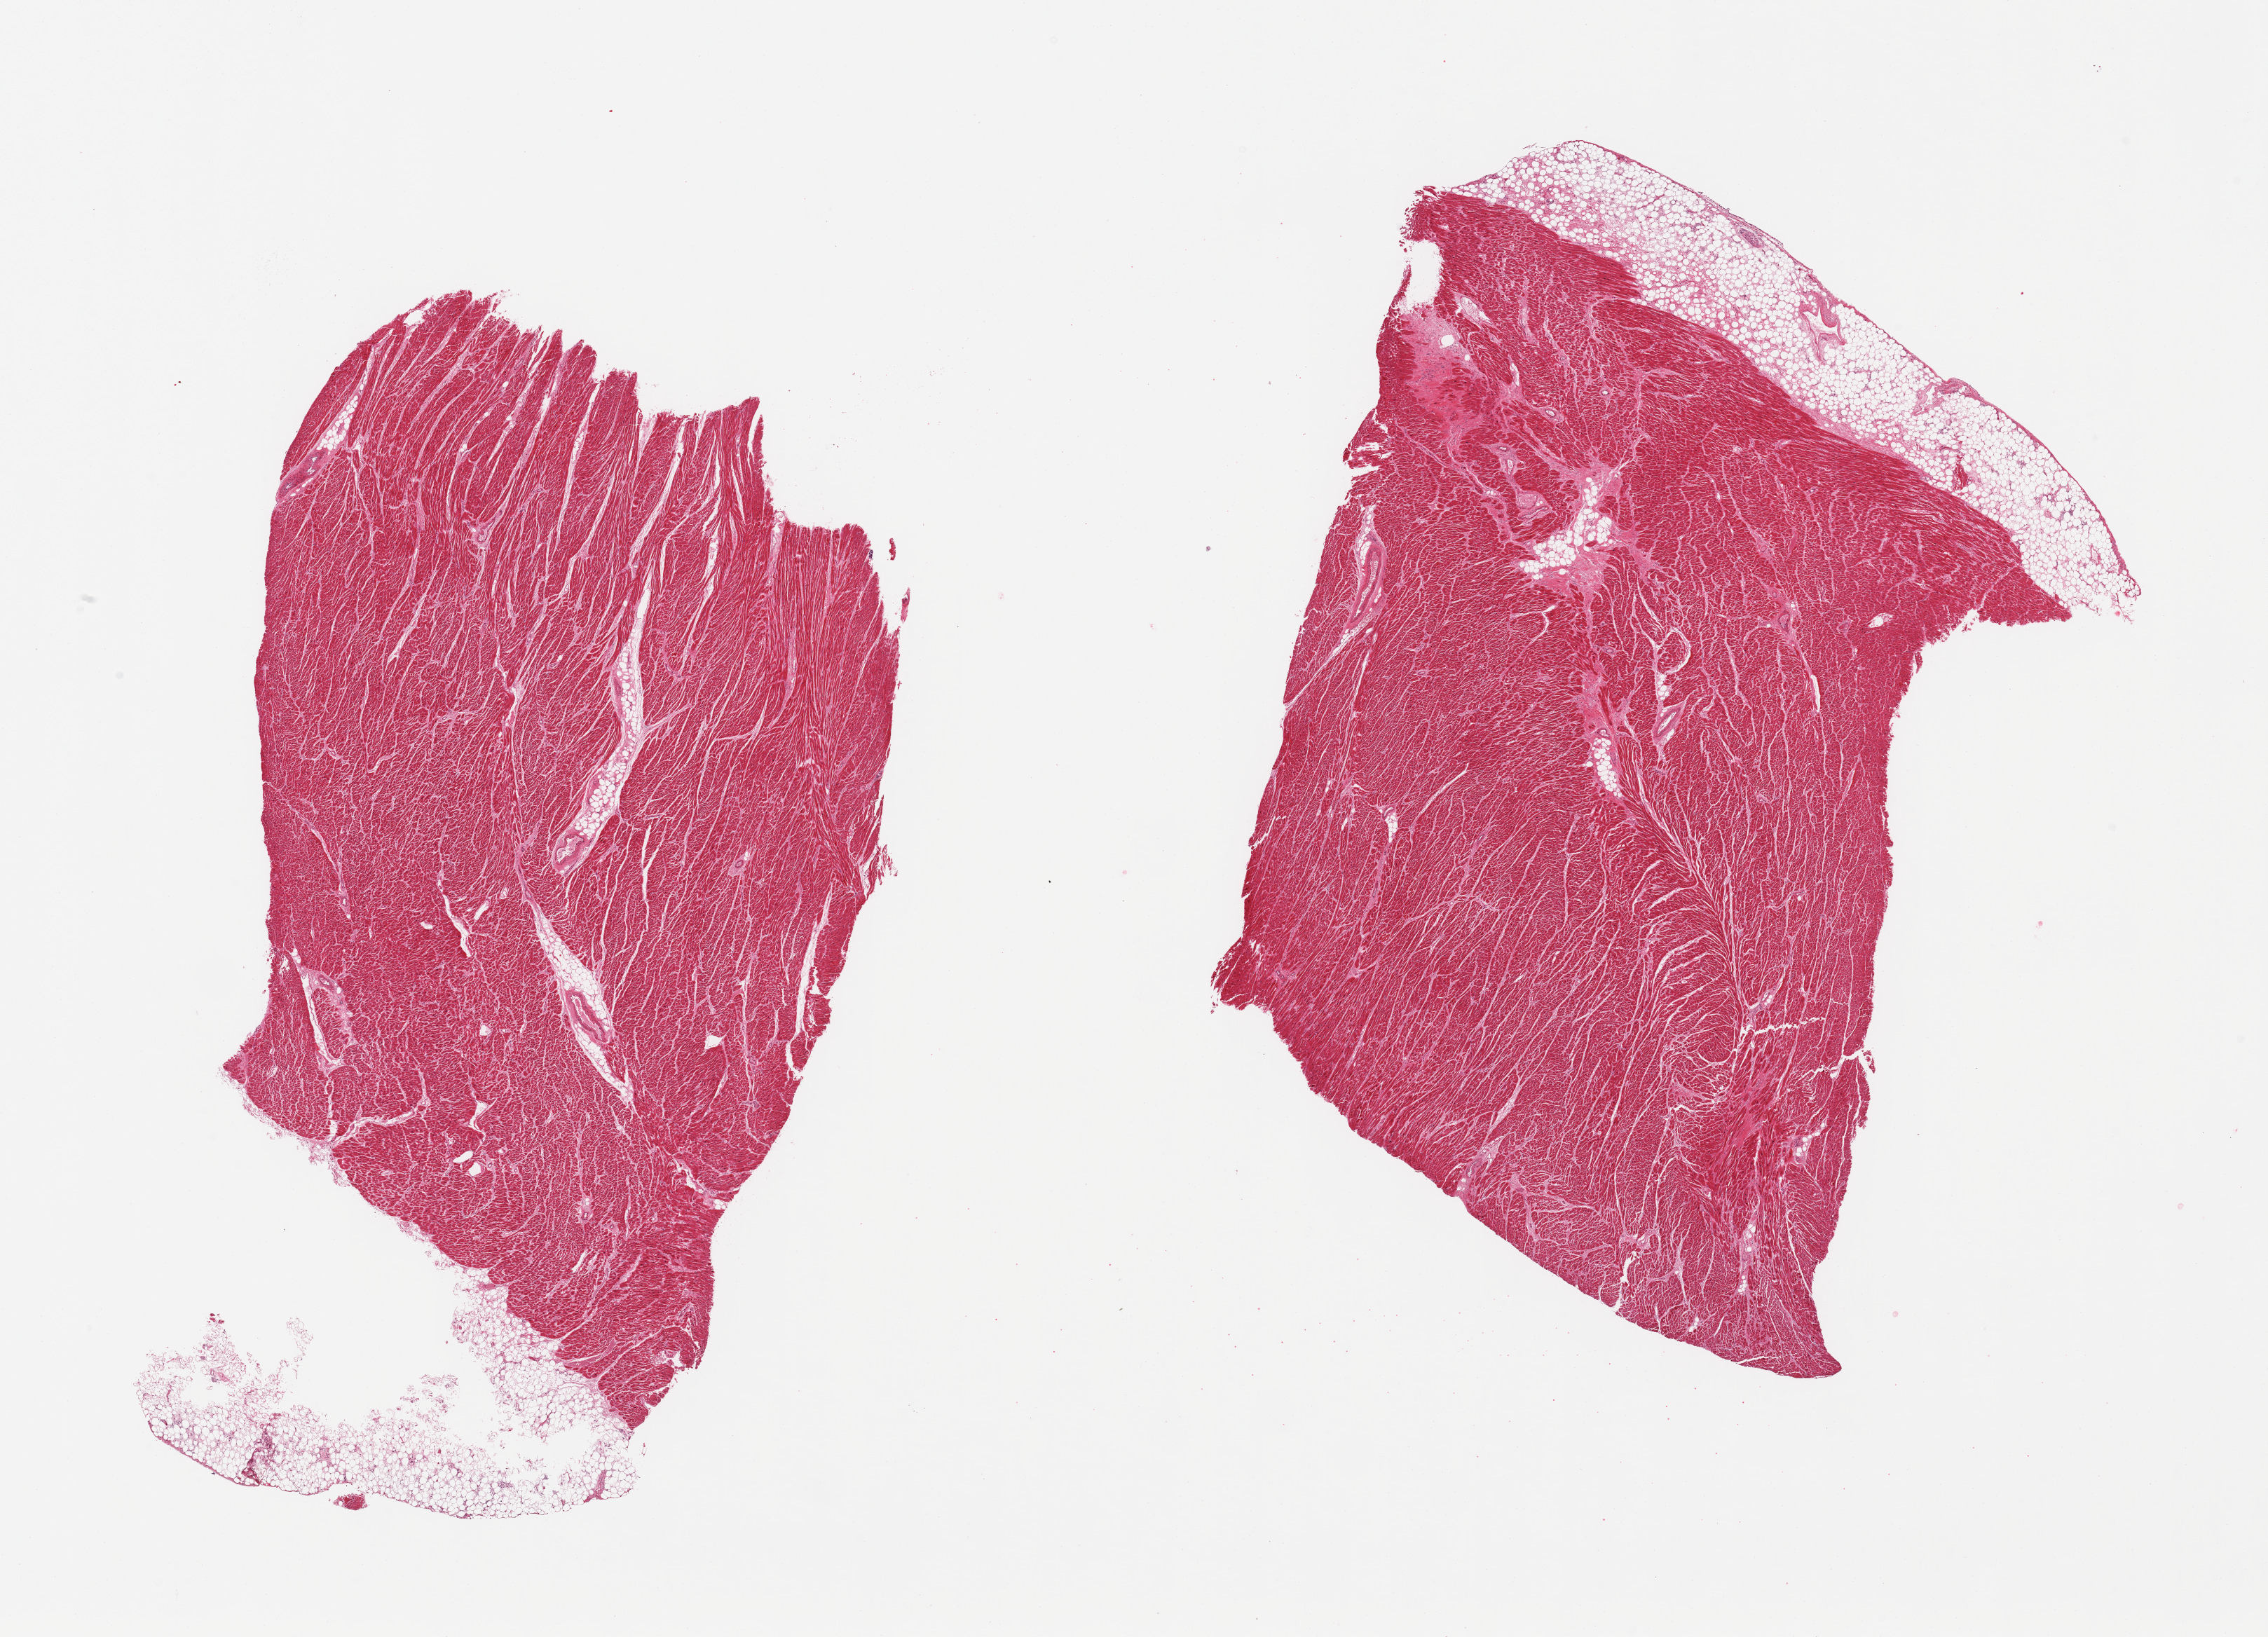
Whole-slide image, hematoxylin and eosin (H&E) stain, brightfield — a low-resolution overview of the entire scanned area, about 25.6 x 18.5 mm; PAXgene-fixed, paraffin-embedded tissue; target tissue: heart; donor tissue sample.
Reviewer comment on this tissue sample: 2 pieces; both include ~10% attached fat, small amount of internal/perivascular fat, patchy areas of scar in one piece.